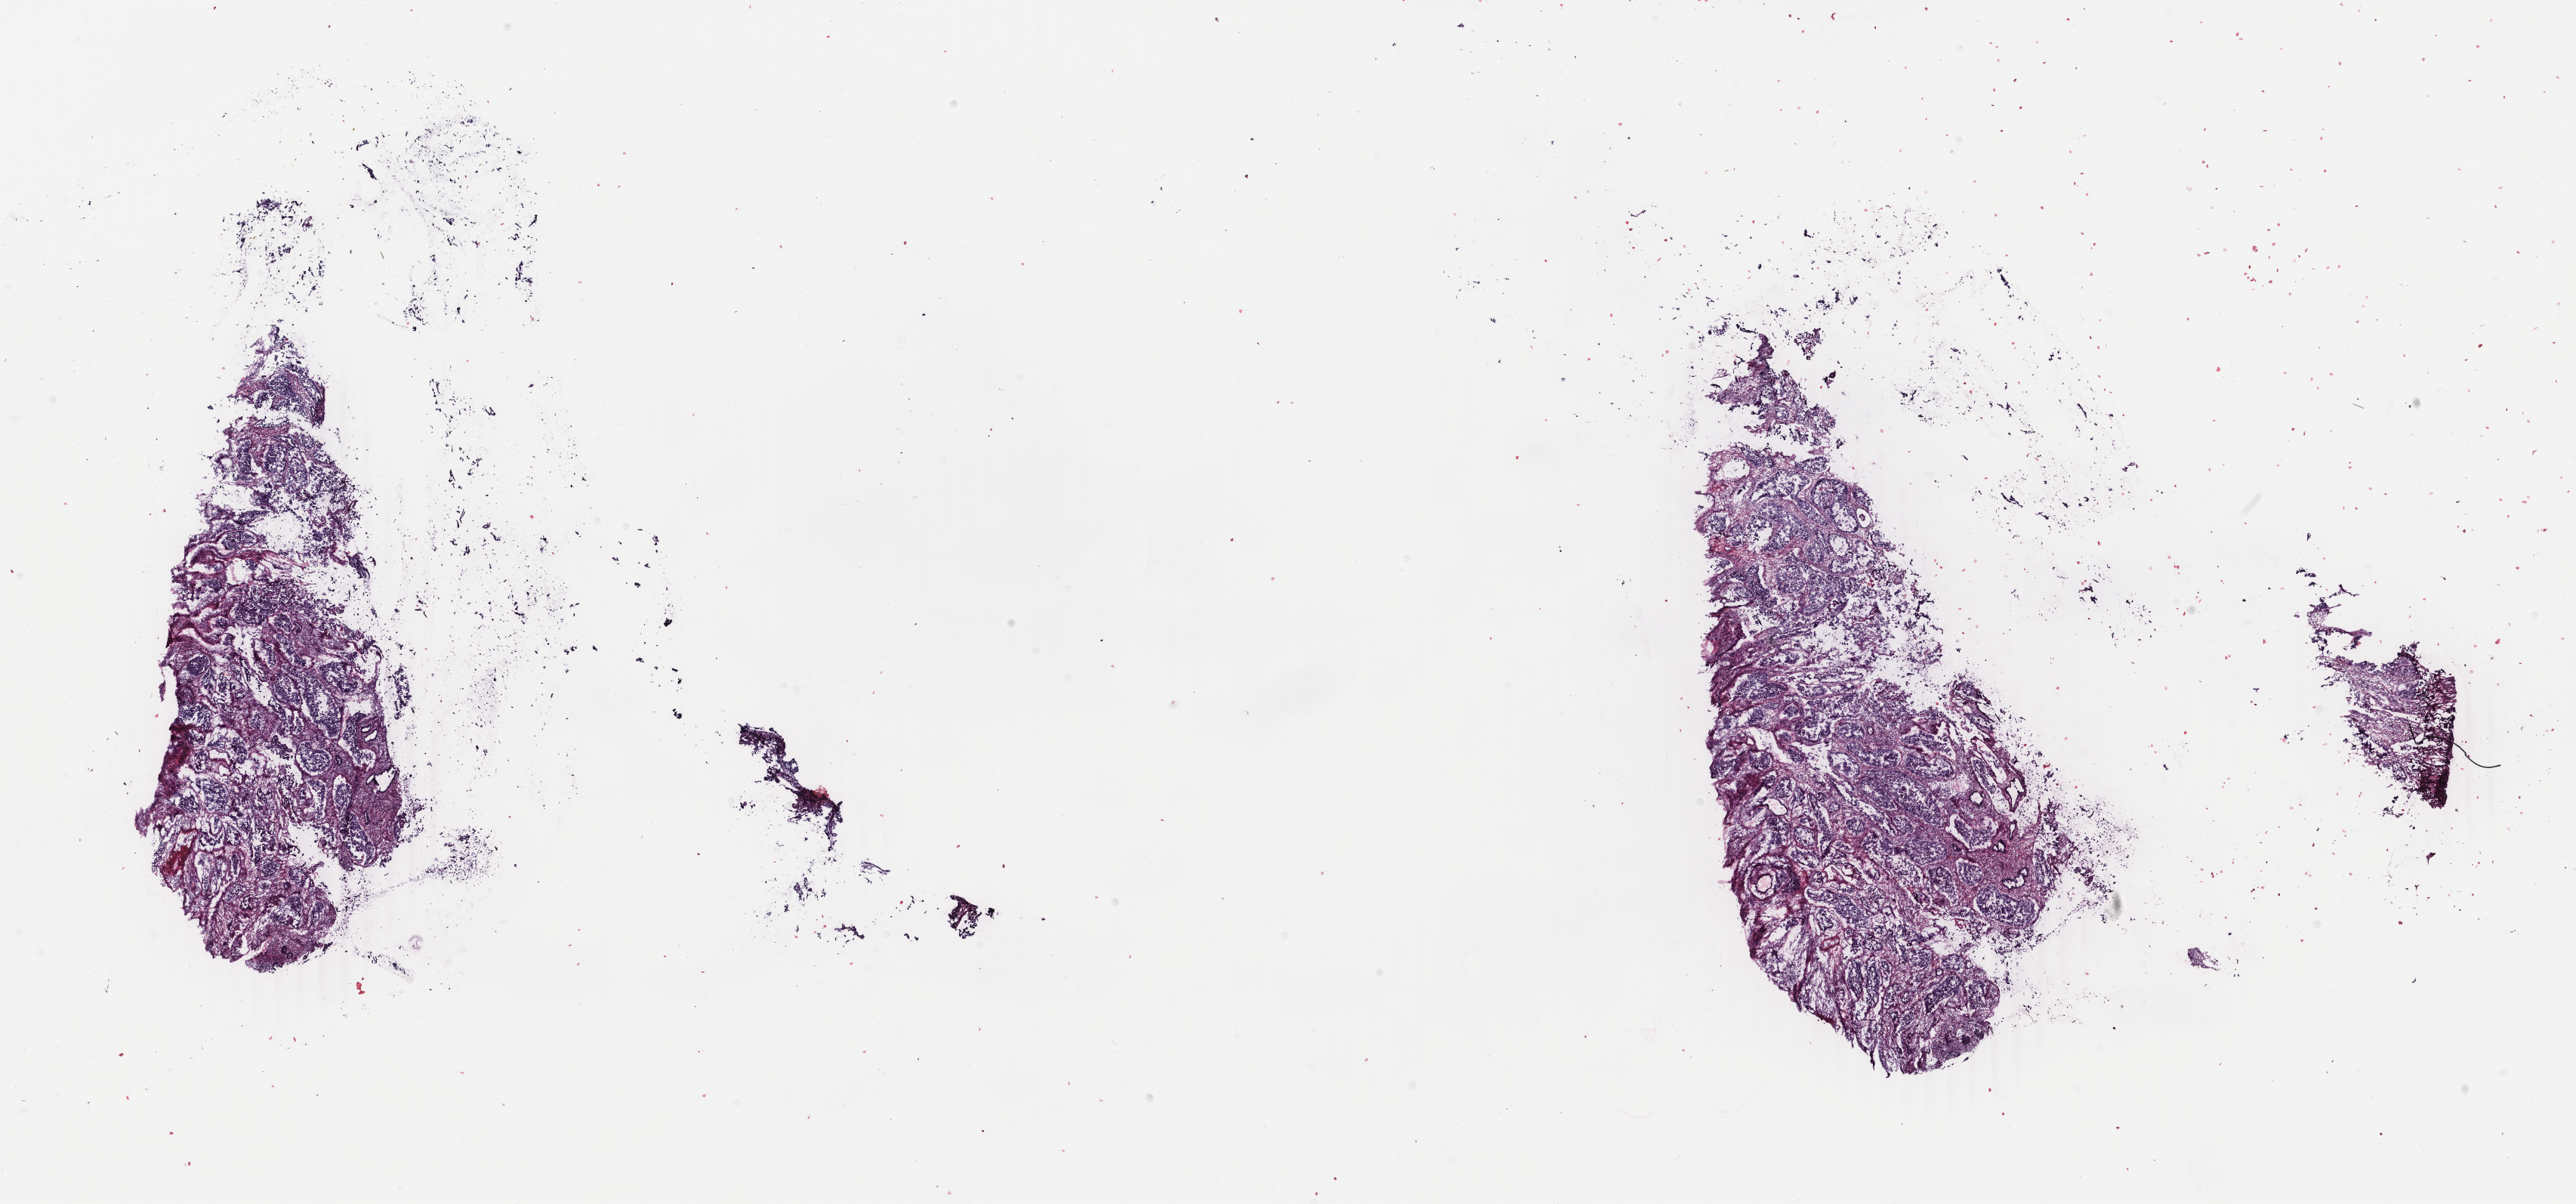
Whole-slide histology image, Hematoxylin and eosin (H&E) stained, shown as a low-resolution overview of the whole scanned area (about 27.1 x 12.7 mm), frozen section from the top of the tissue portion, primary tumour sample from the uterus. Patient: female, age at initial diagnosis 64 years. Histologic grade: G3 (poorly differentiated). Composition of this section per pathologist review: tumour cells 70%, tumour nuclei 70%, normal cells 0%, stromal cells 20%, necrosis 10%. Infiltration values recorded for this section: lymphocyte infiltration 30%, monocyte infiltration 15%, neutrophil infiltration 35%.
* FIGO stage: IIIC1
* pathologic diagnosis: Serous cystadenocarcinoma, NOS (endometrium)
* lymph nodes positive (case pathology): 0 of 3 examined